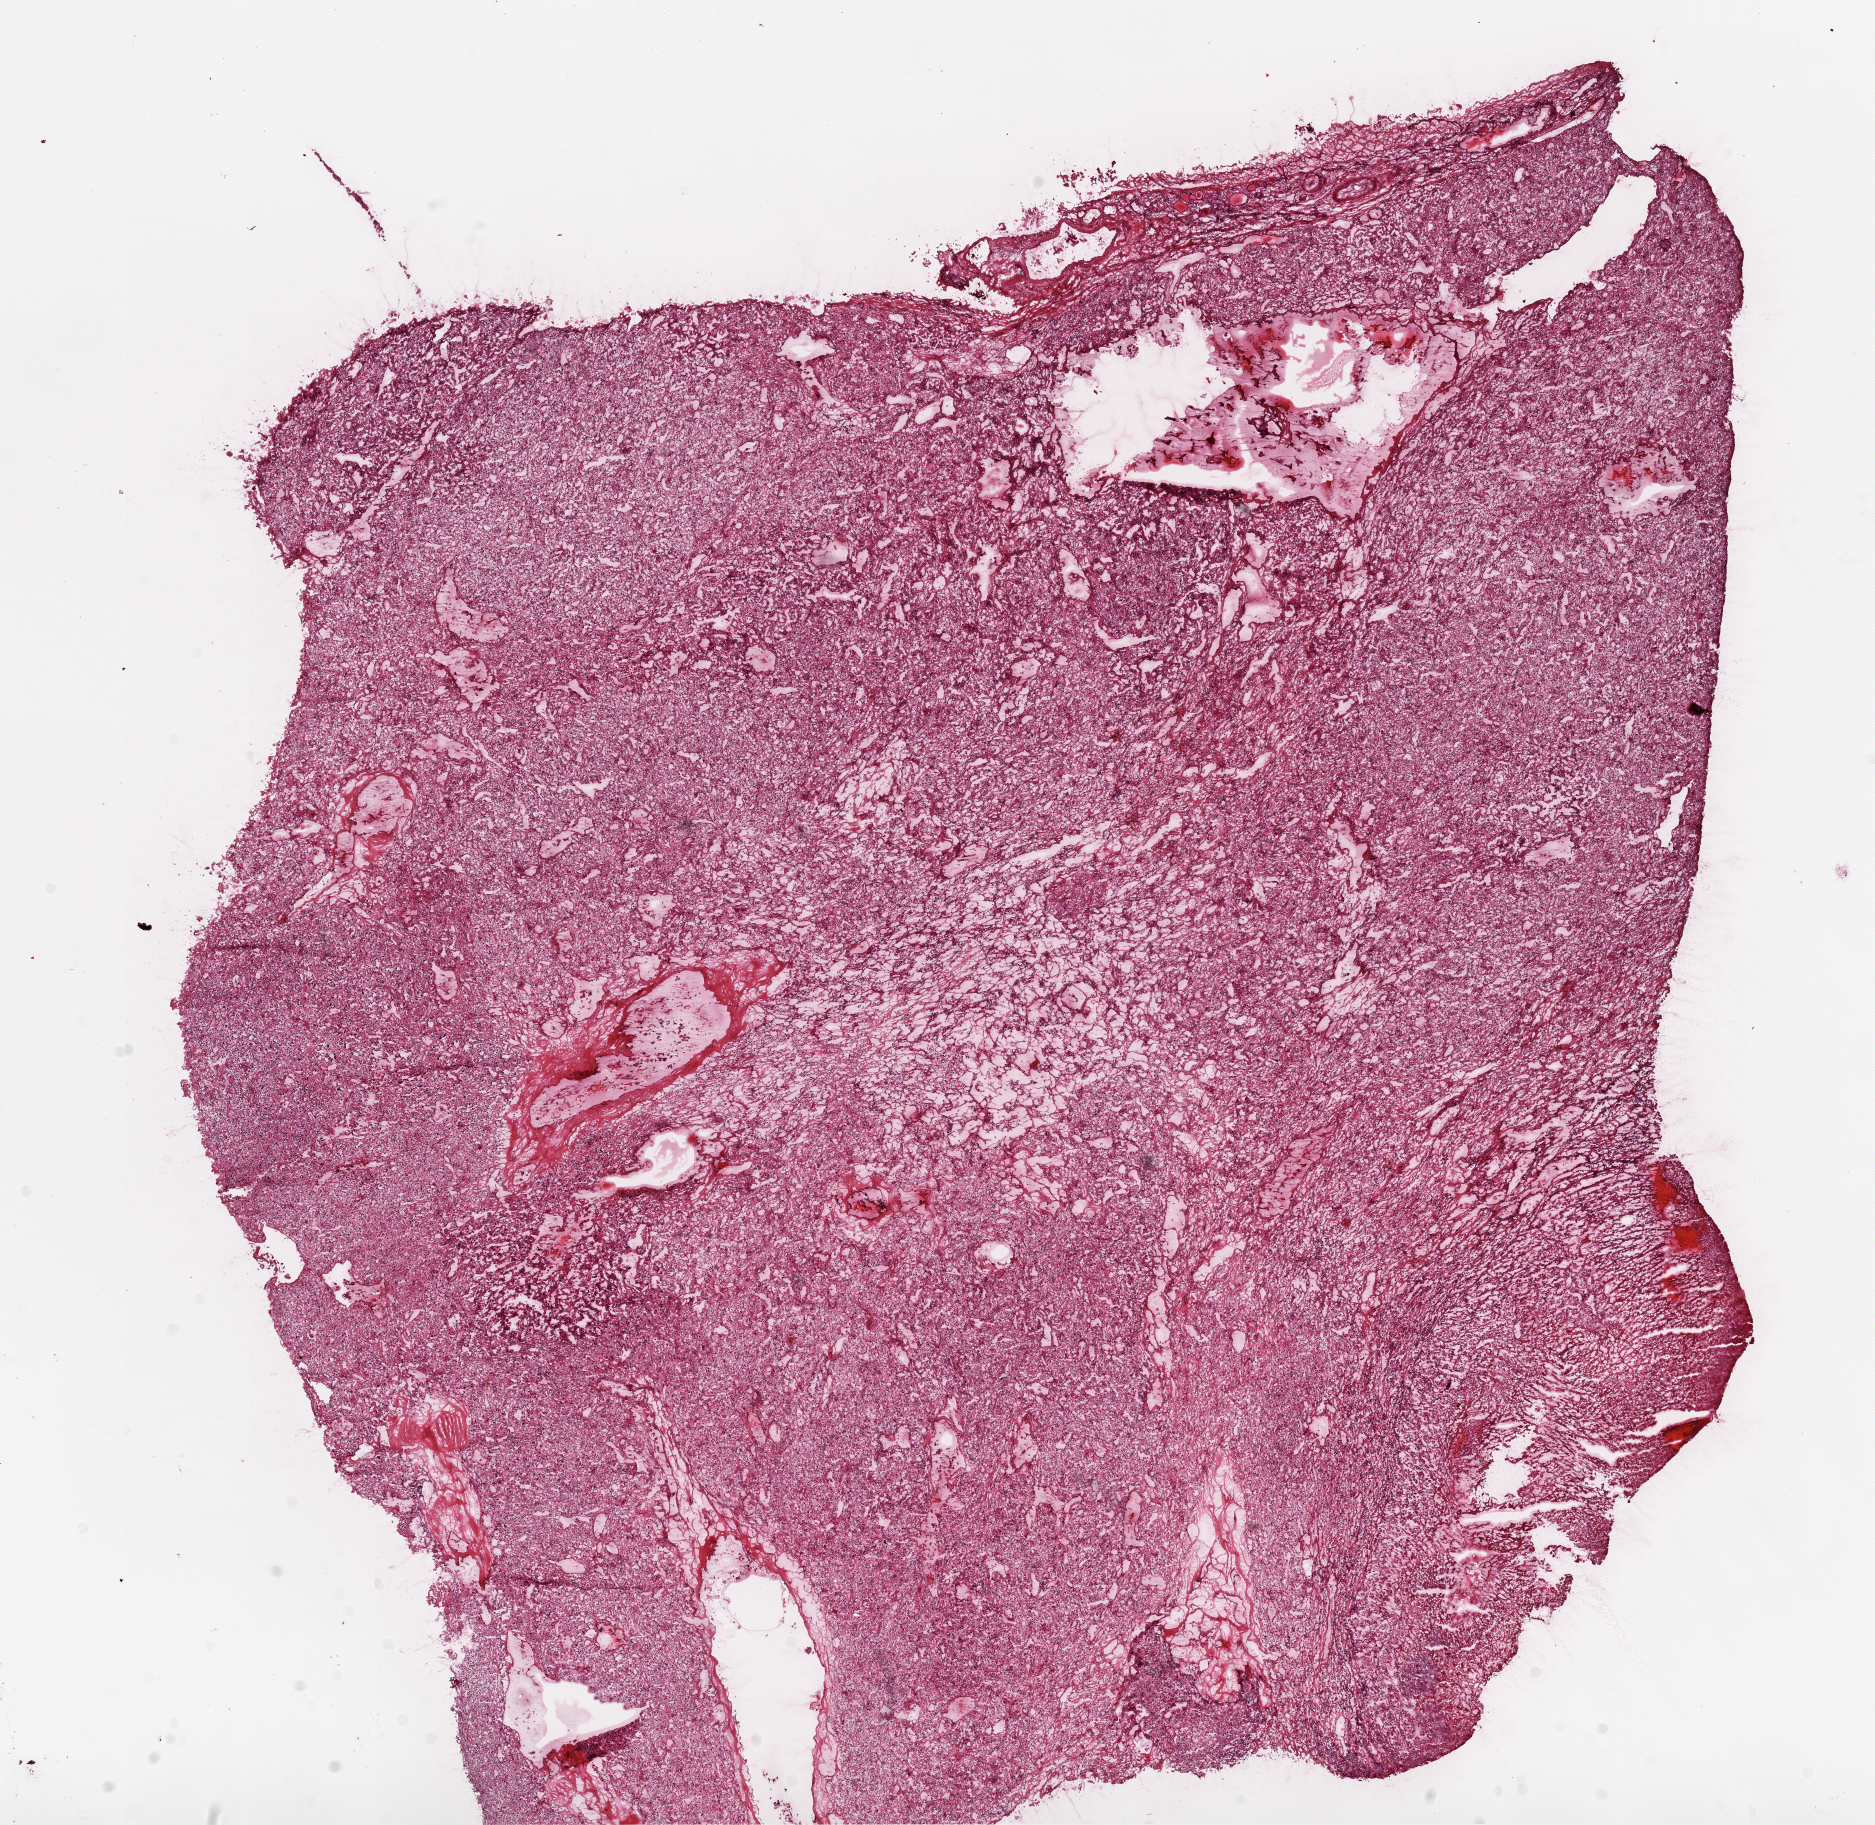
Digitized H&E tissue section (whole slide) — low-resolution overview of the scanned area, about 15.0 x 14.6 mm (from a 20x scan), frozen section from the top of the tissue portion, primary tumour sample from the kidney. Female, age 65 years at initial diagnosis. Histologic grade: G3 (poorly differentiated). Pathologist review of this section (percent, as recorded): tumour cells 90%, tumour nuclei 80%, normal cells 0%, stromal cells 10%, necrosis 0%.
Laterality: left. Diagnosis: Clear cell adenocarcinoma, NOS. AJCC pathologic stage: IV.